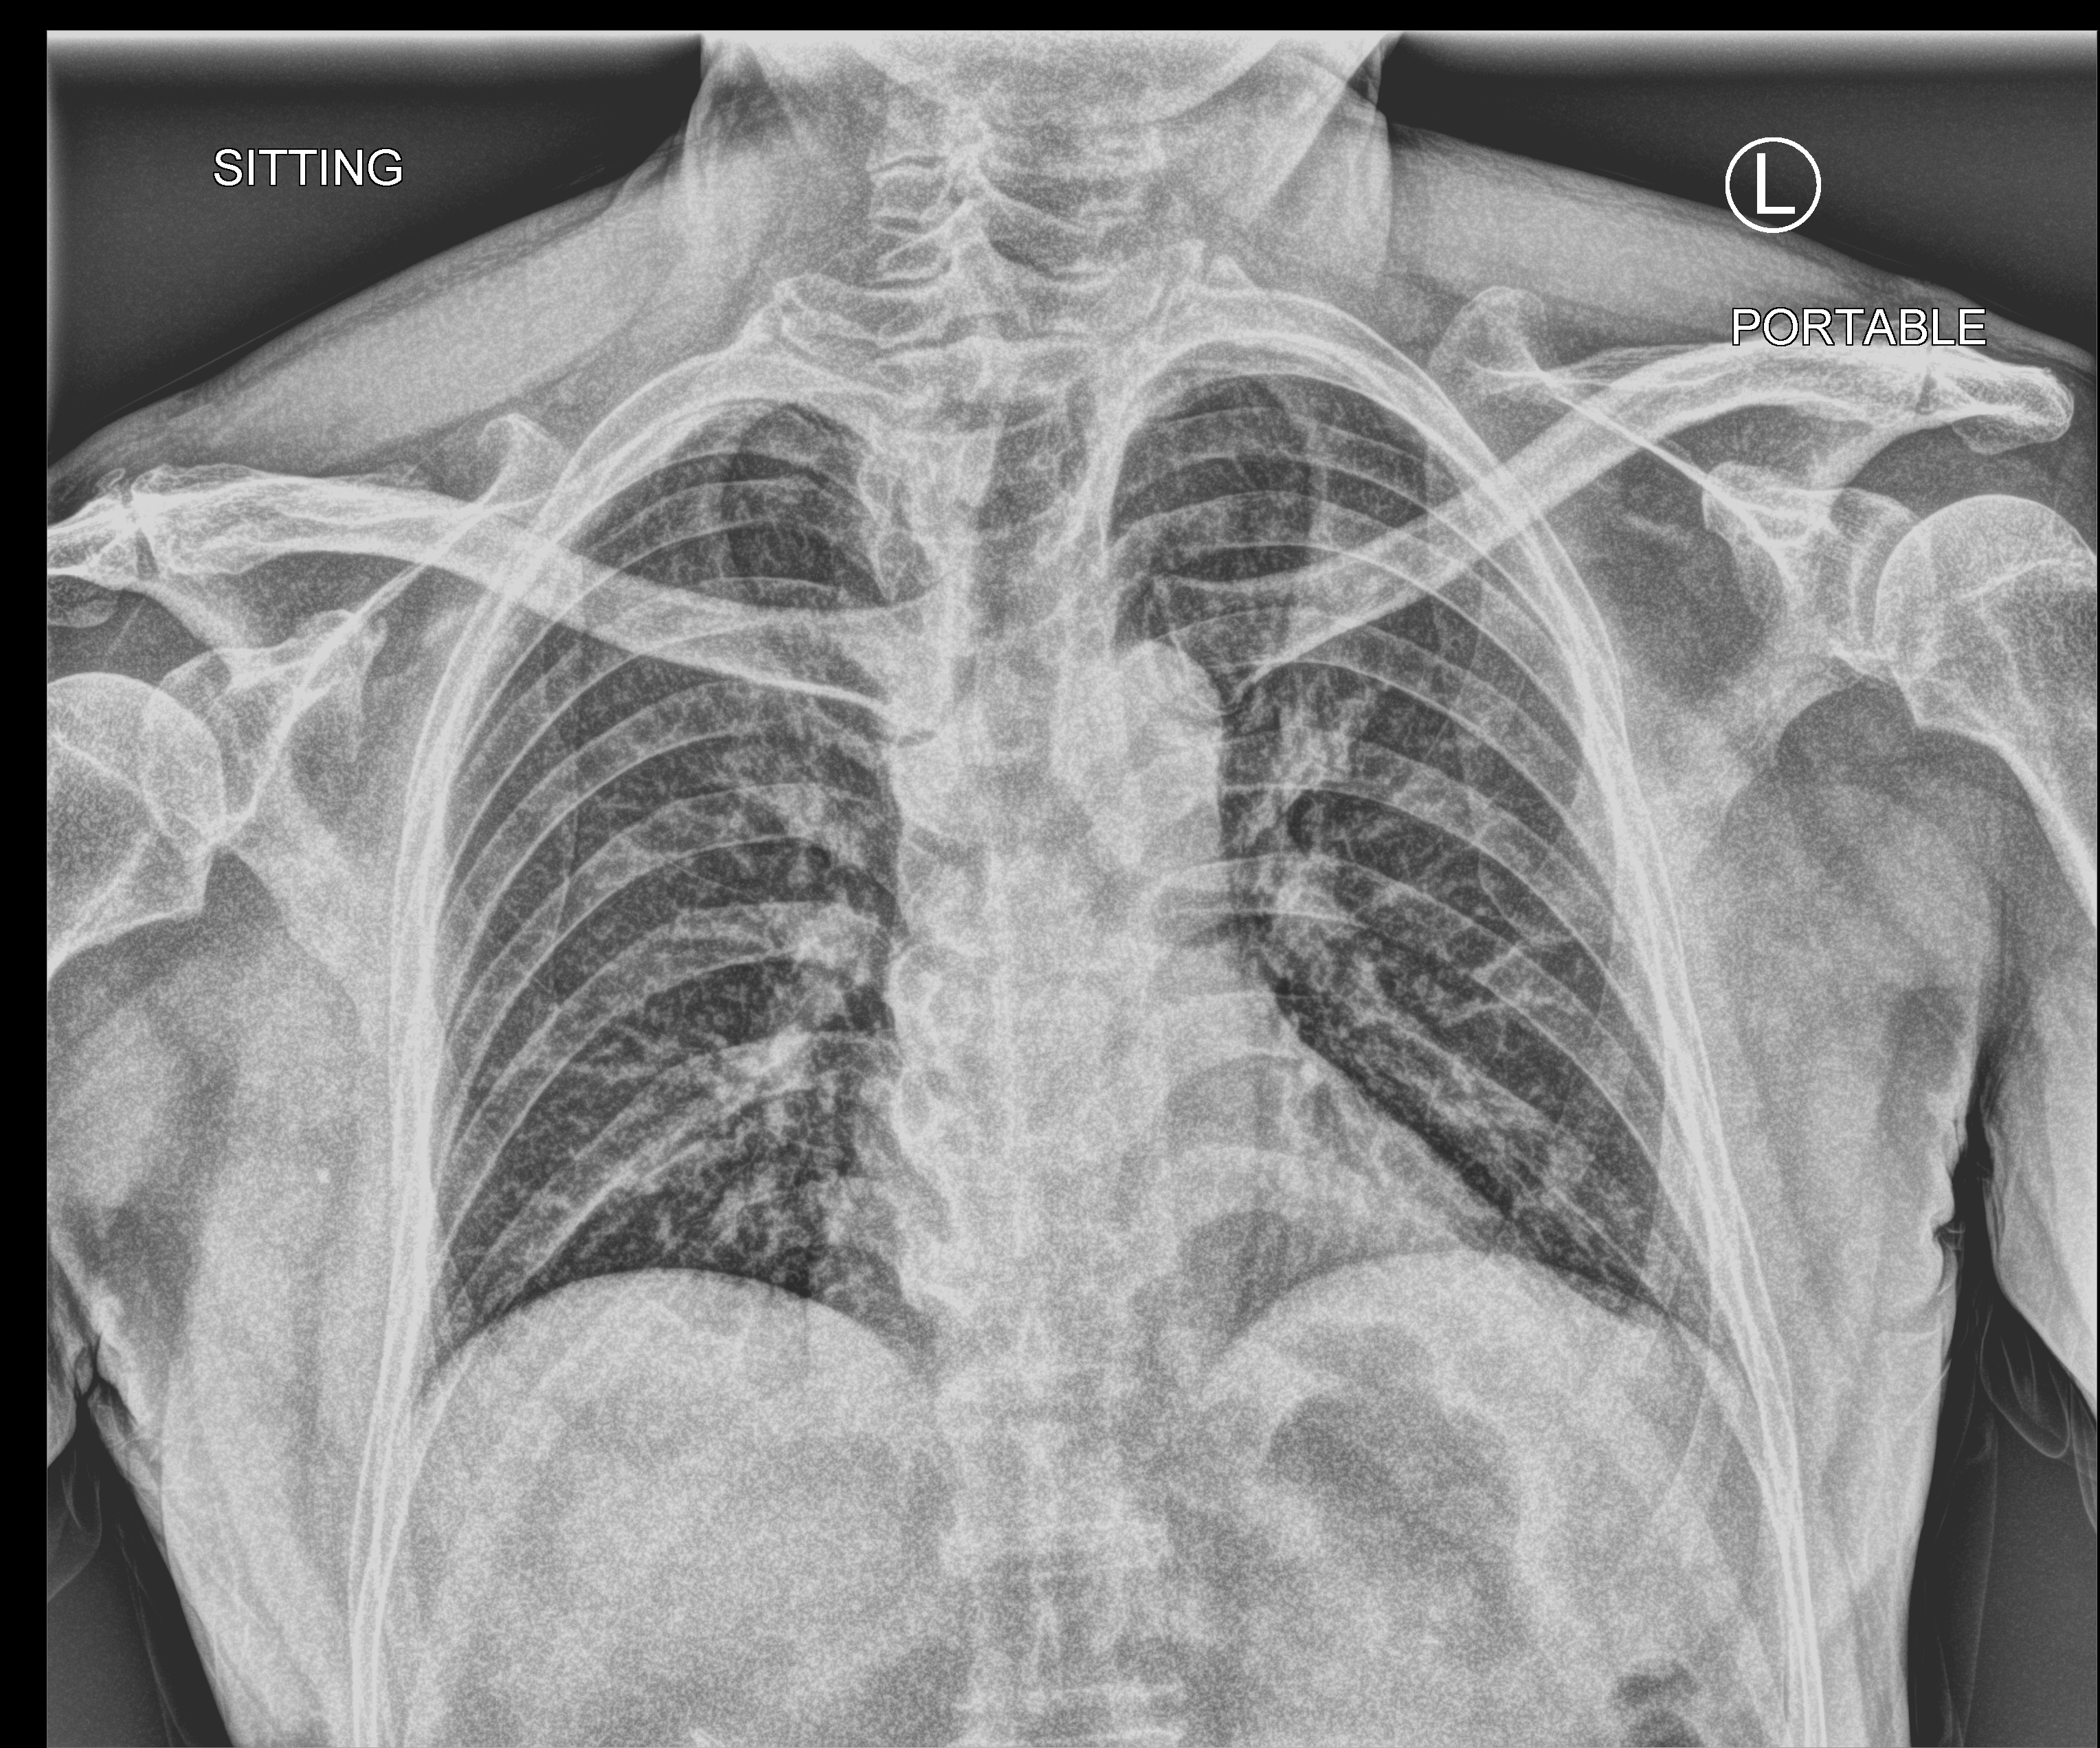
Chest X-ray (portable); anteroposterior (AP) projection. Male patient hospitalised with COVID-19, age 60–74 years.
Admission-level facts for this patient (not findings on this image; timing relative to this image not recorded): admitted to intensive care during this hospital stay: no; mechanically ventilated during this hospital stay: no; hypertension (admission record): no.